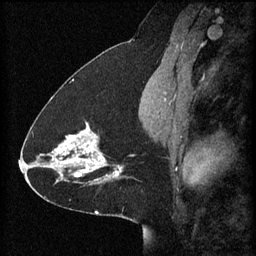
Breast MRI (dynamic contrast-enhanced), one sagittal slice; slice 31 of 60 in the series (ordered by position); 3 images stored at this slice position (order not interpretable as contrast timing); 1.5 T; TE 4.2 ms, TR 8.2 ms; 2 mm slice thickness; 256 × 256 image matrix. Female patient, age 41 years.
Annotated regions visible in this slice (semi-automatic segmentation, software-assisted and operator-edited):
- analysis volume of interest (the breast-tissue region the enhancement analysis was run in; not a lesion): bounding box [x1, y1, x2, y2] px = [58, 122, 125, 181]
- tumour enhancement mask (voxels above the 70 % enhancement threshold inside the analysis volume of interest): [58, 122, 123, 181]